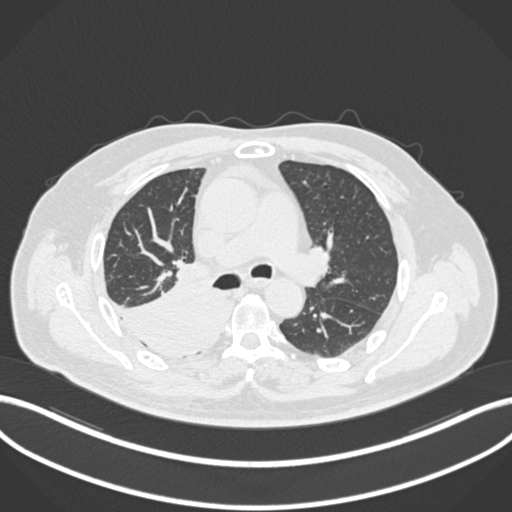
Chest CT, one axial slice; position 124 of 218 along the scan axis; reconstruction kernel B30f; 120 kVp; lung window (W 1500 / L -600 HU); 512 × 512 image matrix, field of view 400 × 400 mm. Patient: male, 68 years. Case-level facts recorded for this patient, not image findings: clinical TNM (as recorded): T2a N0 M0.
Outlined on this slice (rectangle marked by the reading radiologist):
- lung tumour (recorded histology: adenocarcinoma): bounding box <110,269,233,354> (left, top, right, bottom; pixels)